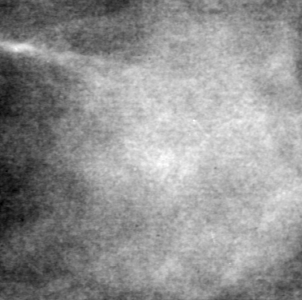
Region of interest cut from a scanned film mammogram (one marked finding), left breast, CC view, BI-RADS breast density category 3 (scale 1–4).
- Marked abnormality: mass, shape round, margins ill defined; BI-RADS assessment category 4; pathology result (as recorded, not read from the image): malignant.